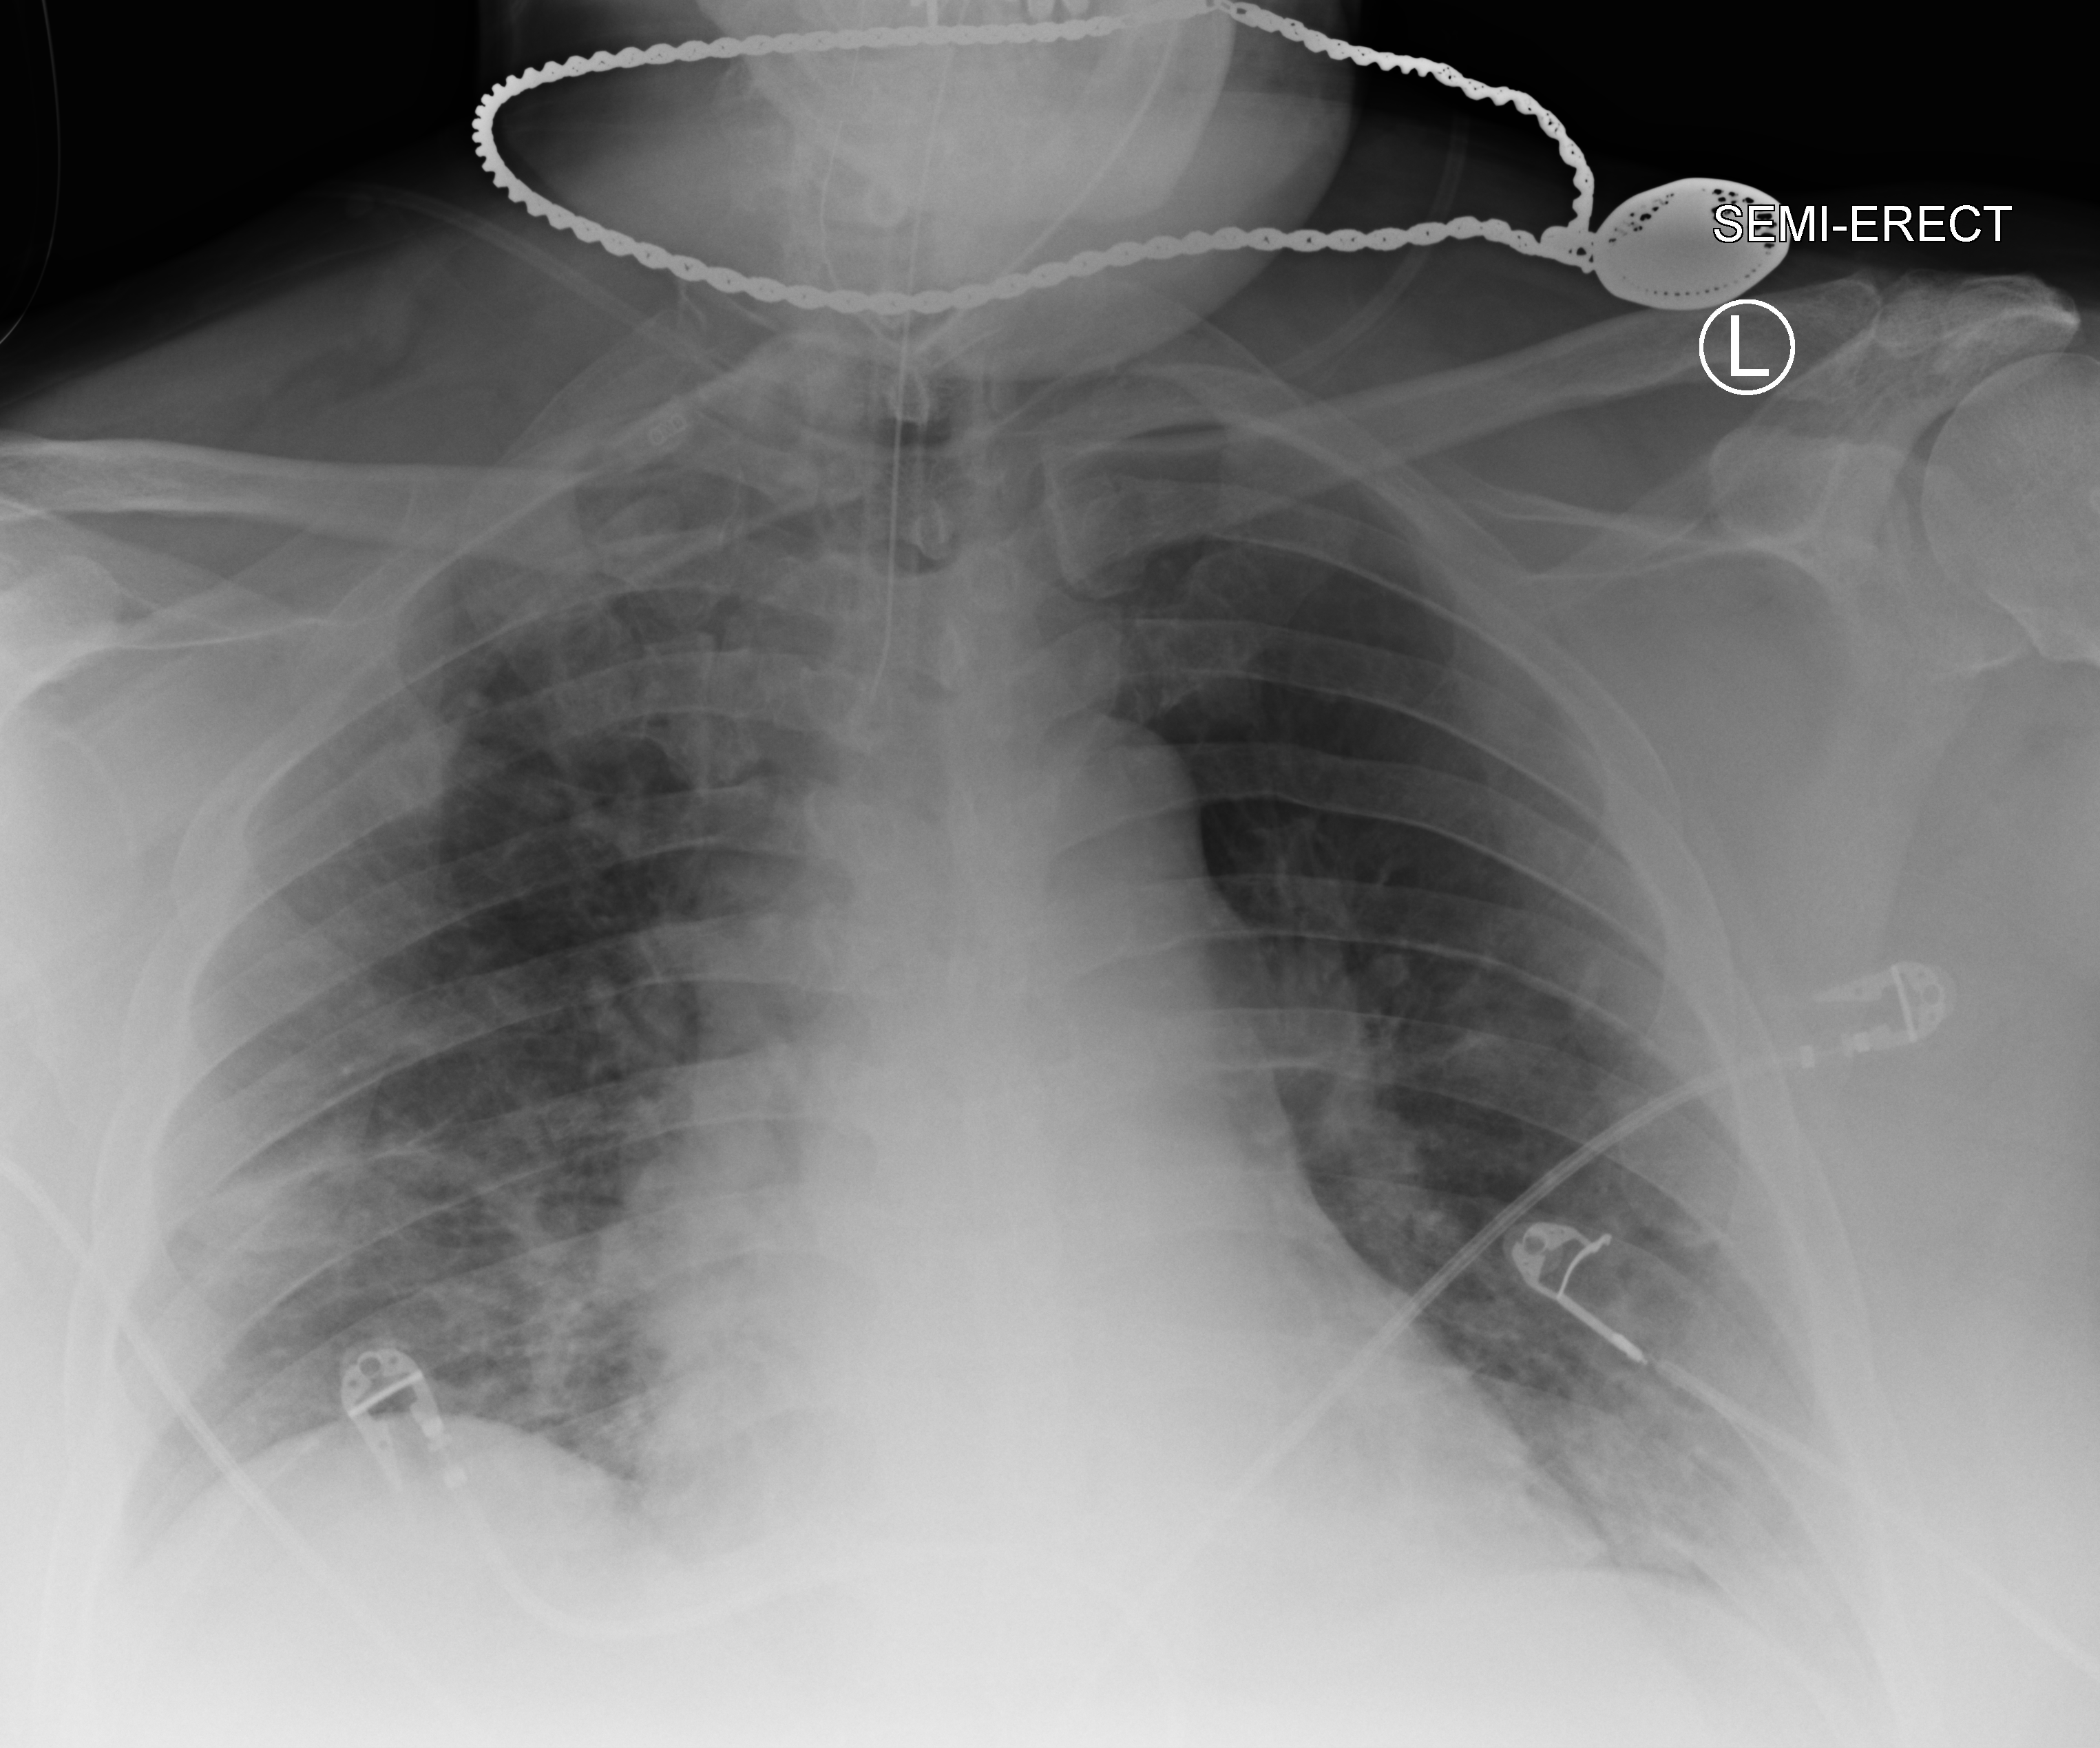
Portable chest radiograph, anteroposterior (AP) projection. Male patient hospitalised with COVID-19, age 60–74 years.
Admission-level facts for this patient (not findings on this image; timing relative to this image not recorded): admitted to intensive care during this hospital stay: no; other chronic lung disease (admission record): no.